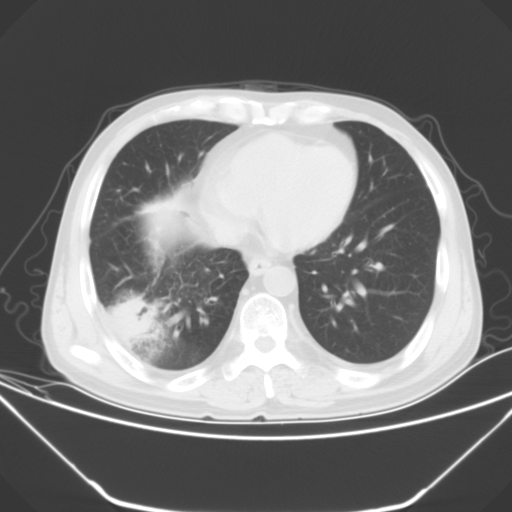
Chest CT, one axial slice. Slice 16 of 52 in the series (ordered by position). 120 kVp. Lung window (W 1500 / L -600 HU). 5 mm slice thickness. 512 × 512 image matrix. Male patient, age 54 years. Case-level facts recorded for this patient, not image findings: clinical TNM (as recorded): T2 N1 M0; histopathological grade: G3.
Structures marked on this image (bounding box drawn by a radiologist):
- lung tumour (recorded histology: adenocarcinoma): bounding box (x1, y1, x2, y2) in pixels: (111, 295, 158, 341)